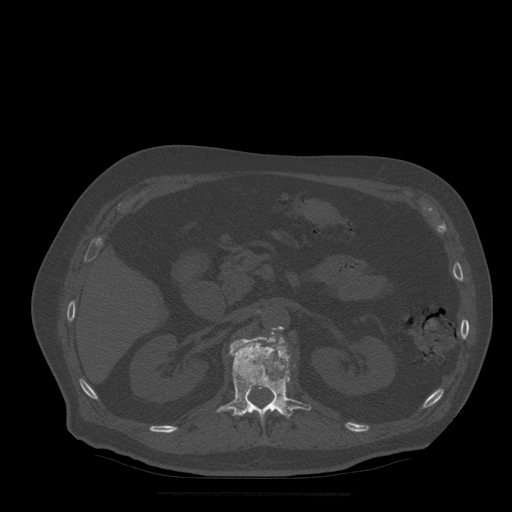
CT including the spine, one axial slice. Position 197 of 522 along the scan axis. Bone window (W 1800 / L 400 HU). 1.25 mm slice thickness. 512 × 512 image matrix, field of view 420 × 420 mm. Patient age 72 years. From the clinical record (not read from this slice): primary cancer: prostate.
Annotated regions visible in this slice (semi-automatically segmented with operator editing):
- L1 vertebra: bounding box [x1, y1, x2, y2] px = [217, 336, 312, 420]
- L2 vertebra: [271, 332, 275, 335]